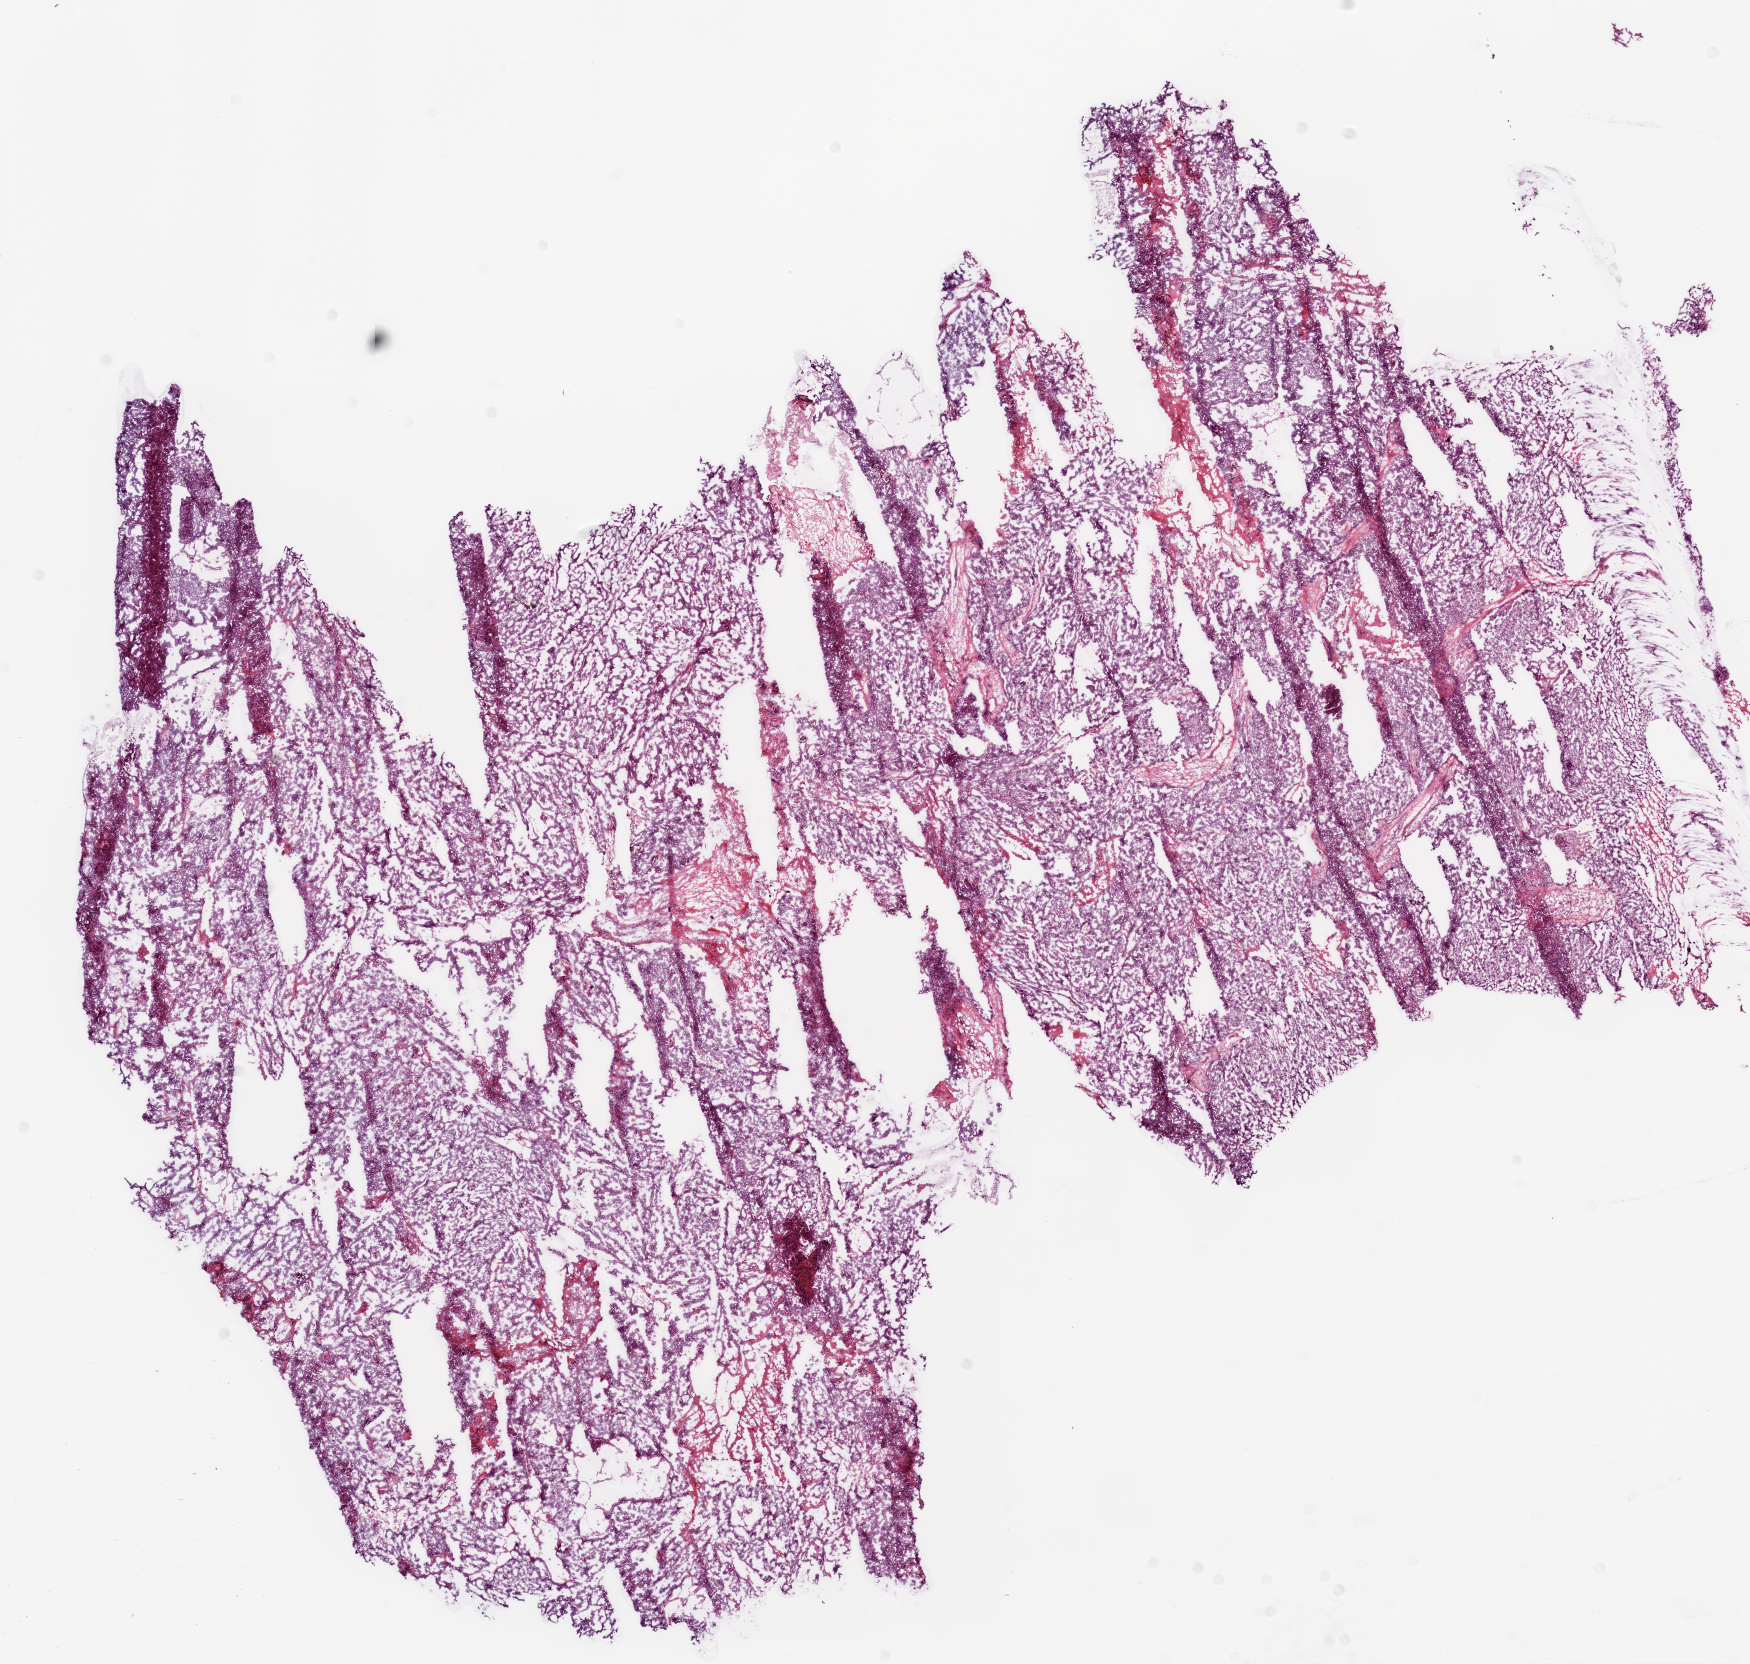
H&E whole-slide image — a low-resolution overview of the entire scanned area, about 14.0 x 13.4 mm (from a 20x scan), frozen section, ovary, primary tumour sample. Female, age 74 years at initial diagnosis. Histologic grade: G3 (poorly differentiated). Pathologist review of this section (percent, as recorded): tumour cells 90%, tumour nuclei 90%, normal cells 0%, stromal cells 10%, necrosis 0%. Infiltration values recorded for this section: lymphocyte infiltration 0%, monocyte infiltration 0%, neutrophil infiltration 0%.
FIGO stage: IIIC. Pathologic diagnosis: Serous cystadenocarcinoma, NOS.